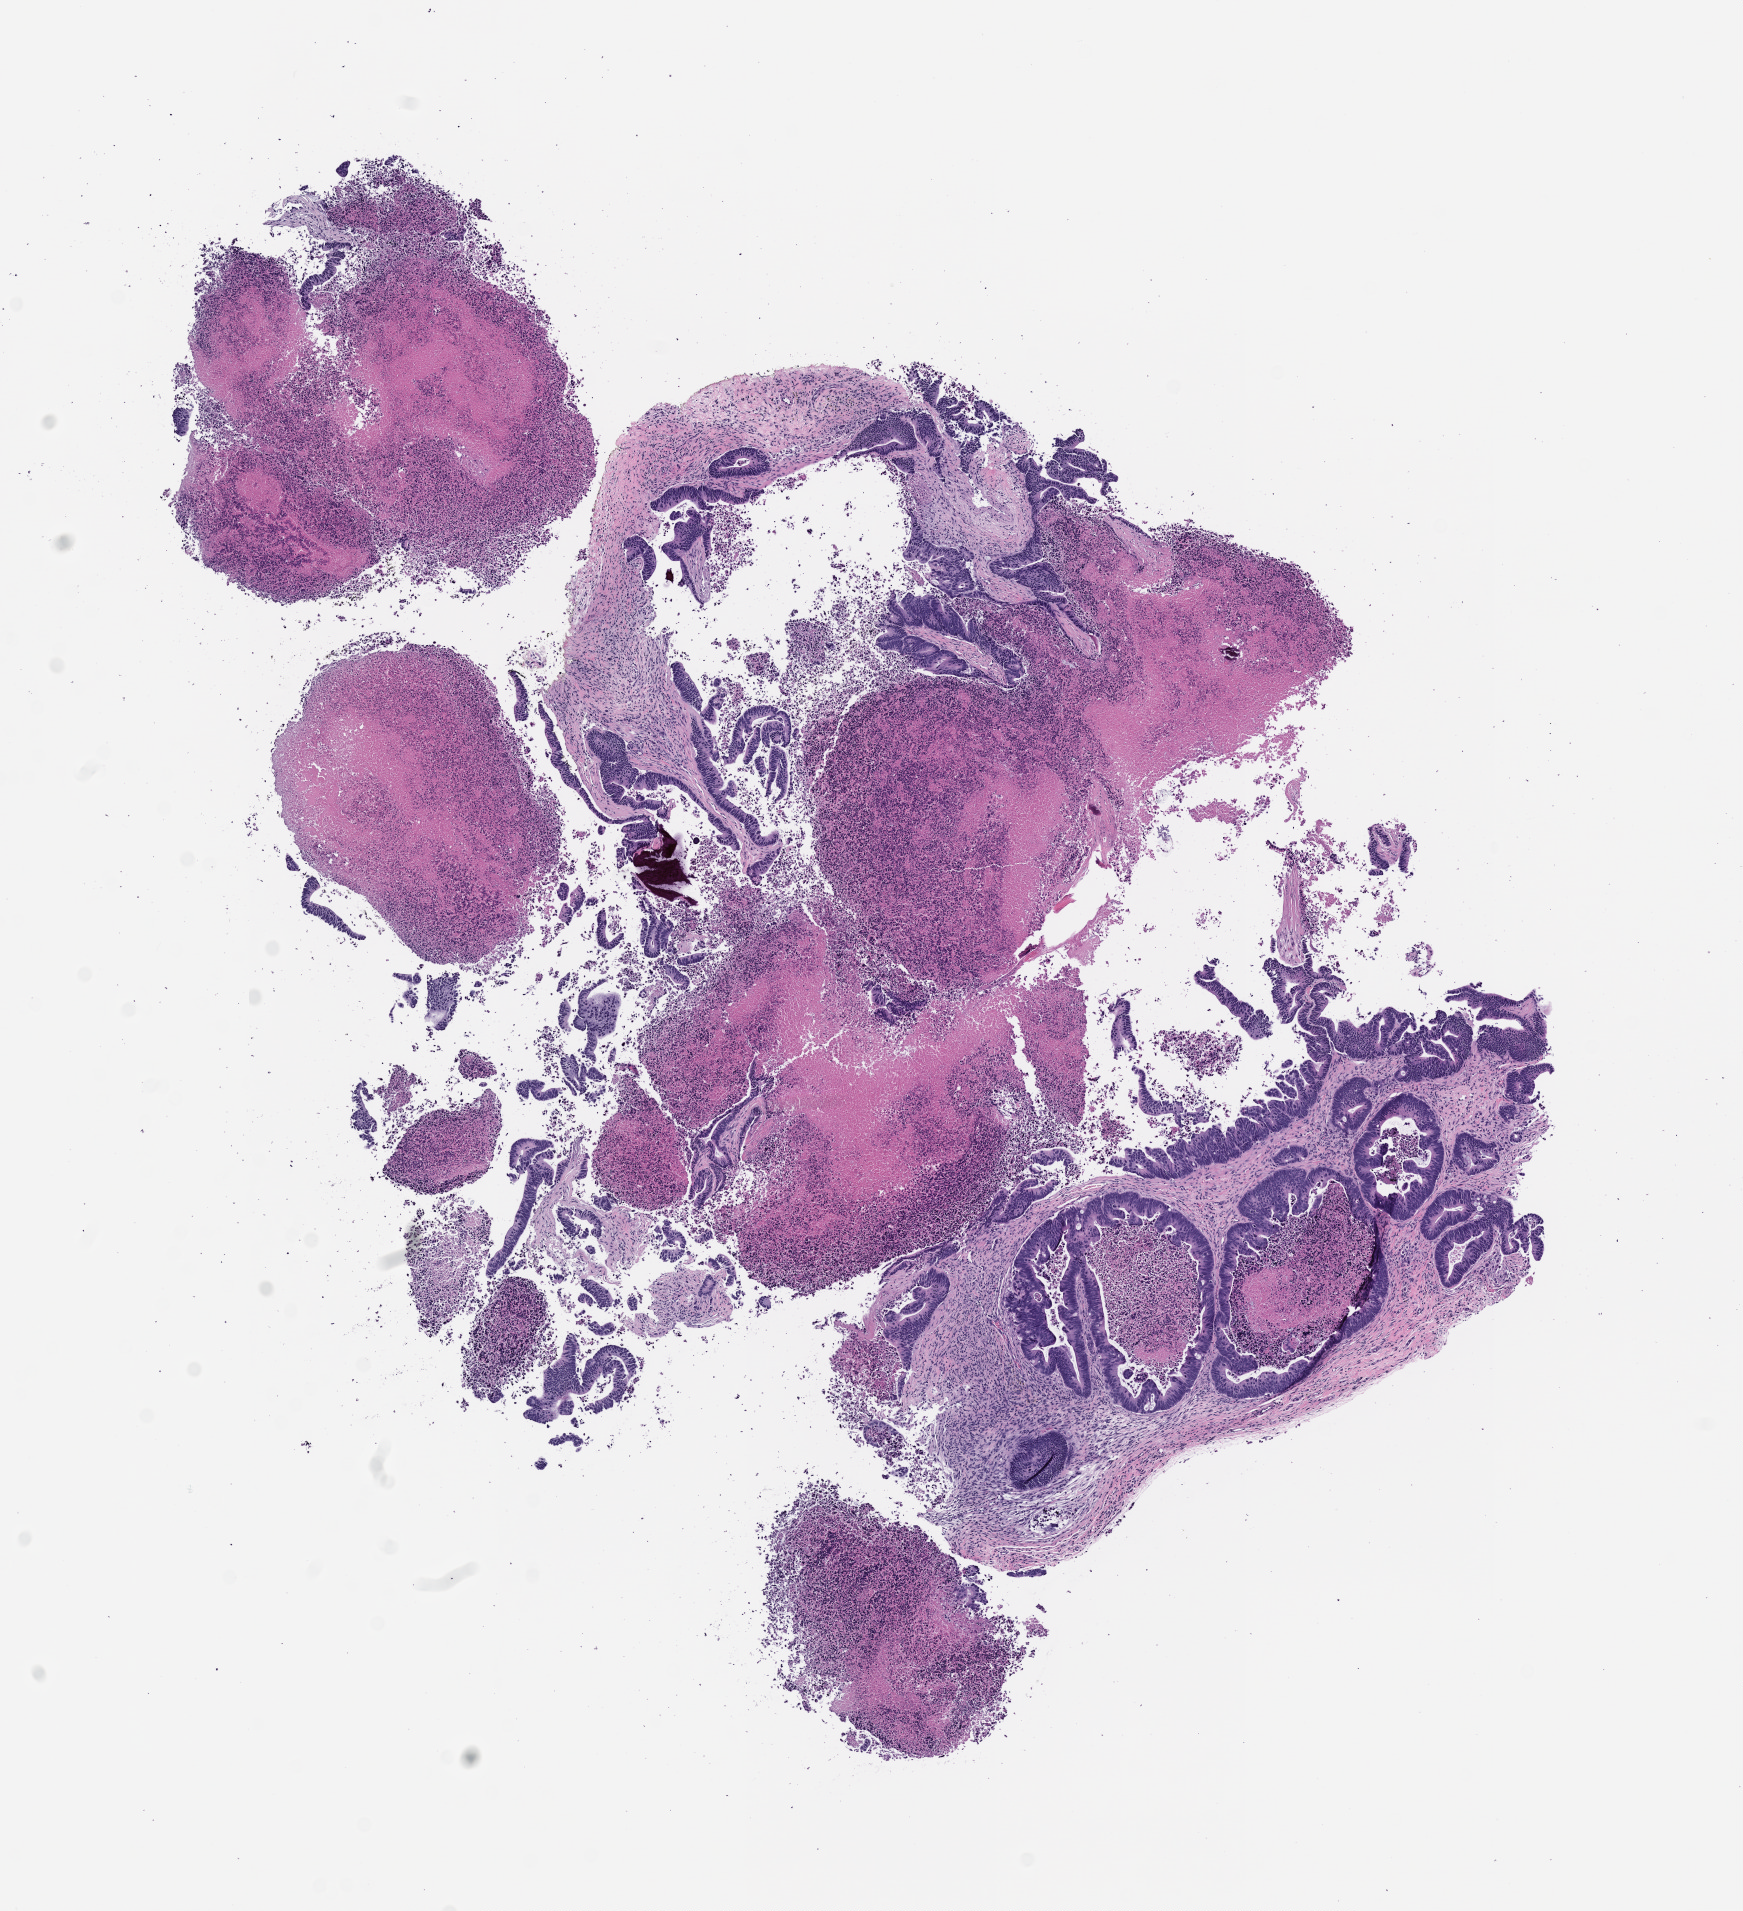
Haematoxylin and eosin whole-slide image of a patient-derived xenograft (PDX) tumor grown in a mouse, passage 2, shown as a low-resolution overview of the whole scanned area (about 7.0 x 7.7 mm). Formalin-fixed, paraffin-embedded (FFPE) tissue. Tumor site category: colon.
Originating patient diagnosis: Colon Adenocarcinoma.